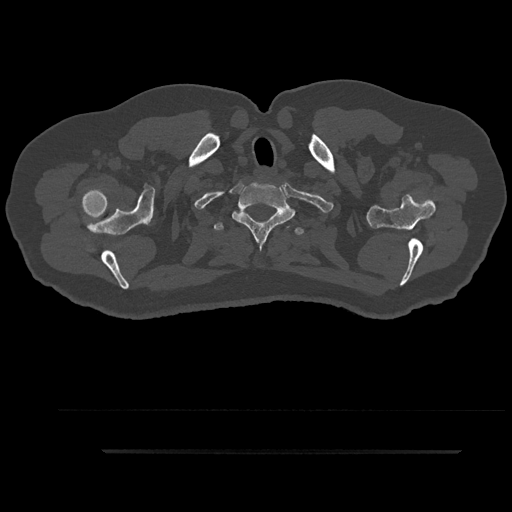
CT including the spine, one axial slice; slice 793 of 797 in the series (ordered by position); 120 kVp; bone window (W 1800 / L 400 HU); 0.5 mm slice thickness; 512 × 512 image matrix, field of view 432 × 432 mm. Male patient, age 63 years. From the clinical record (not read from this slice): primary cancer: renal.
Structures marked on this image (semi-automatic segmentation, software-assisted and operator-edited):
- T1 vertebra: bounding box (x1, y1, x2, y2) in pixels: (232, 185, 297, 249)
- T2 vertebra: (214, 222, 305, 236)